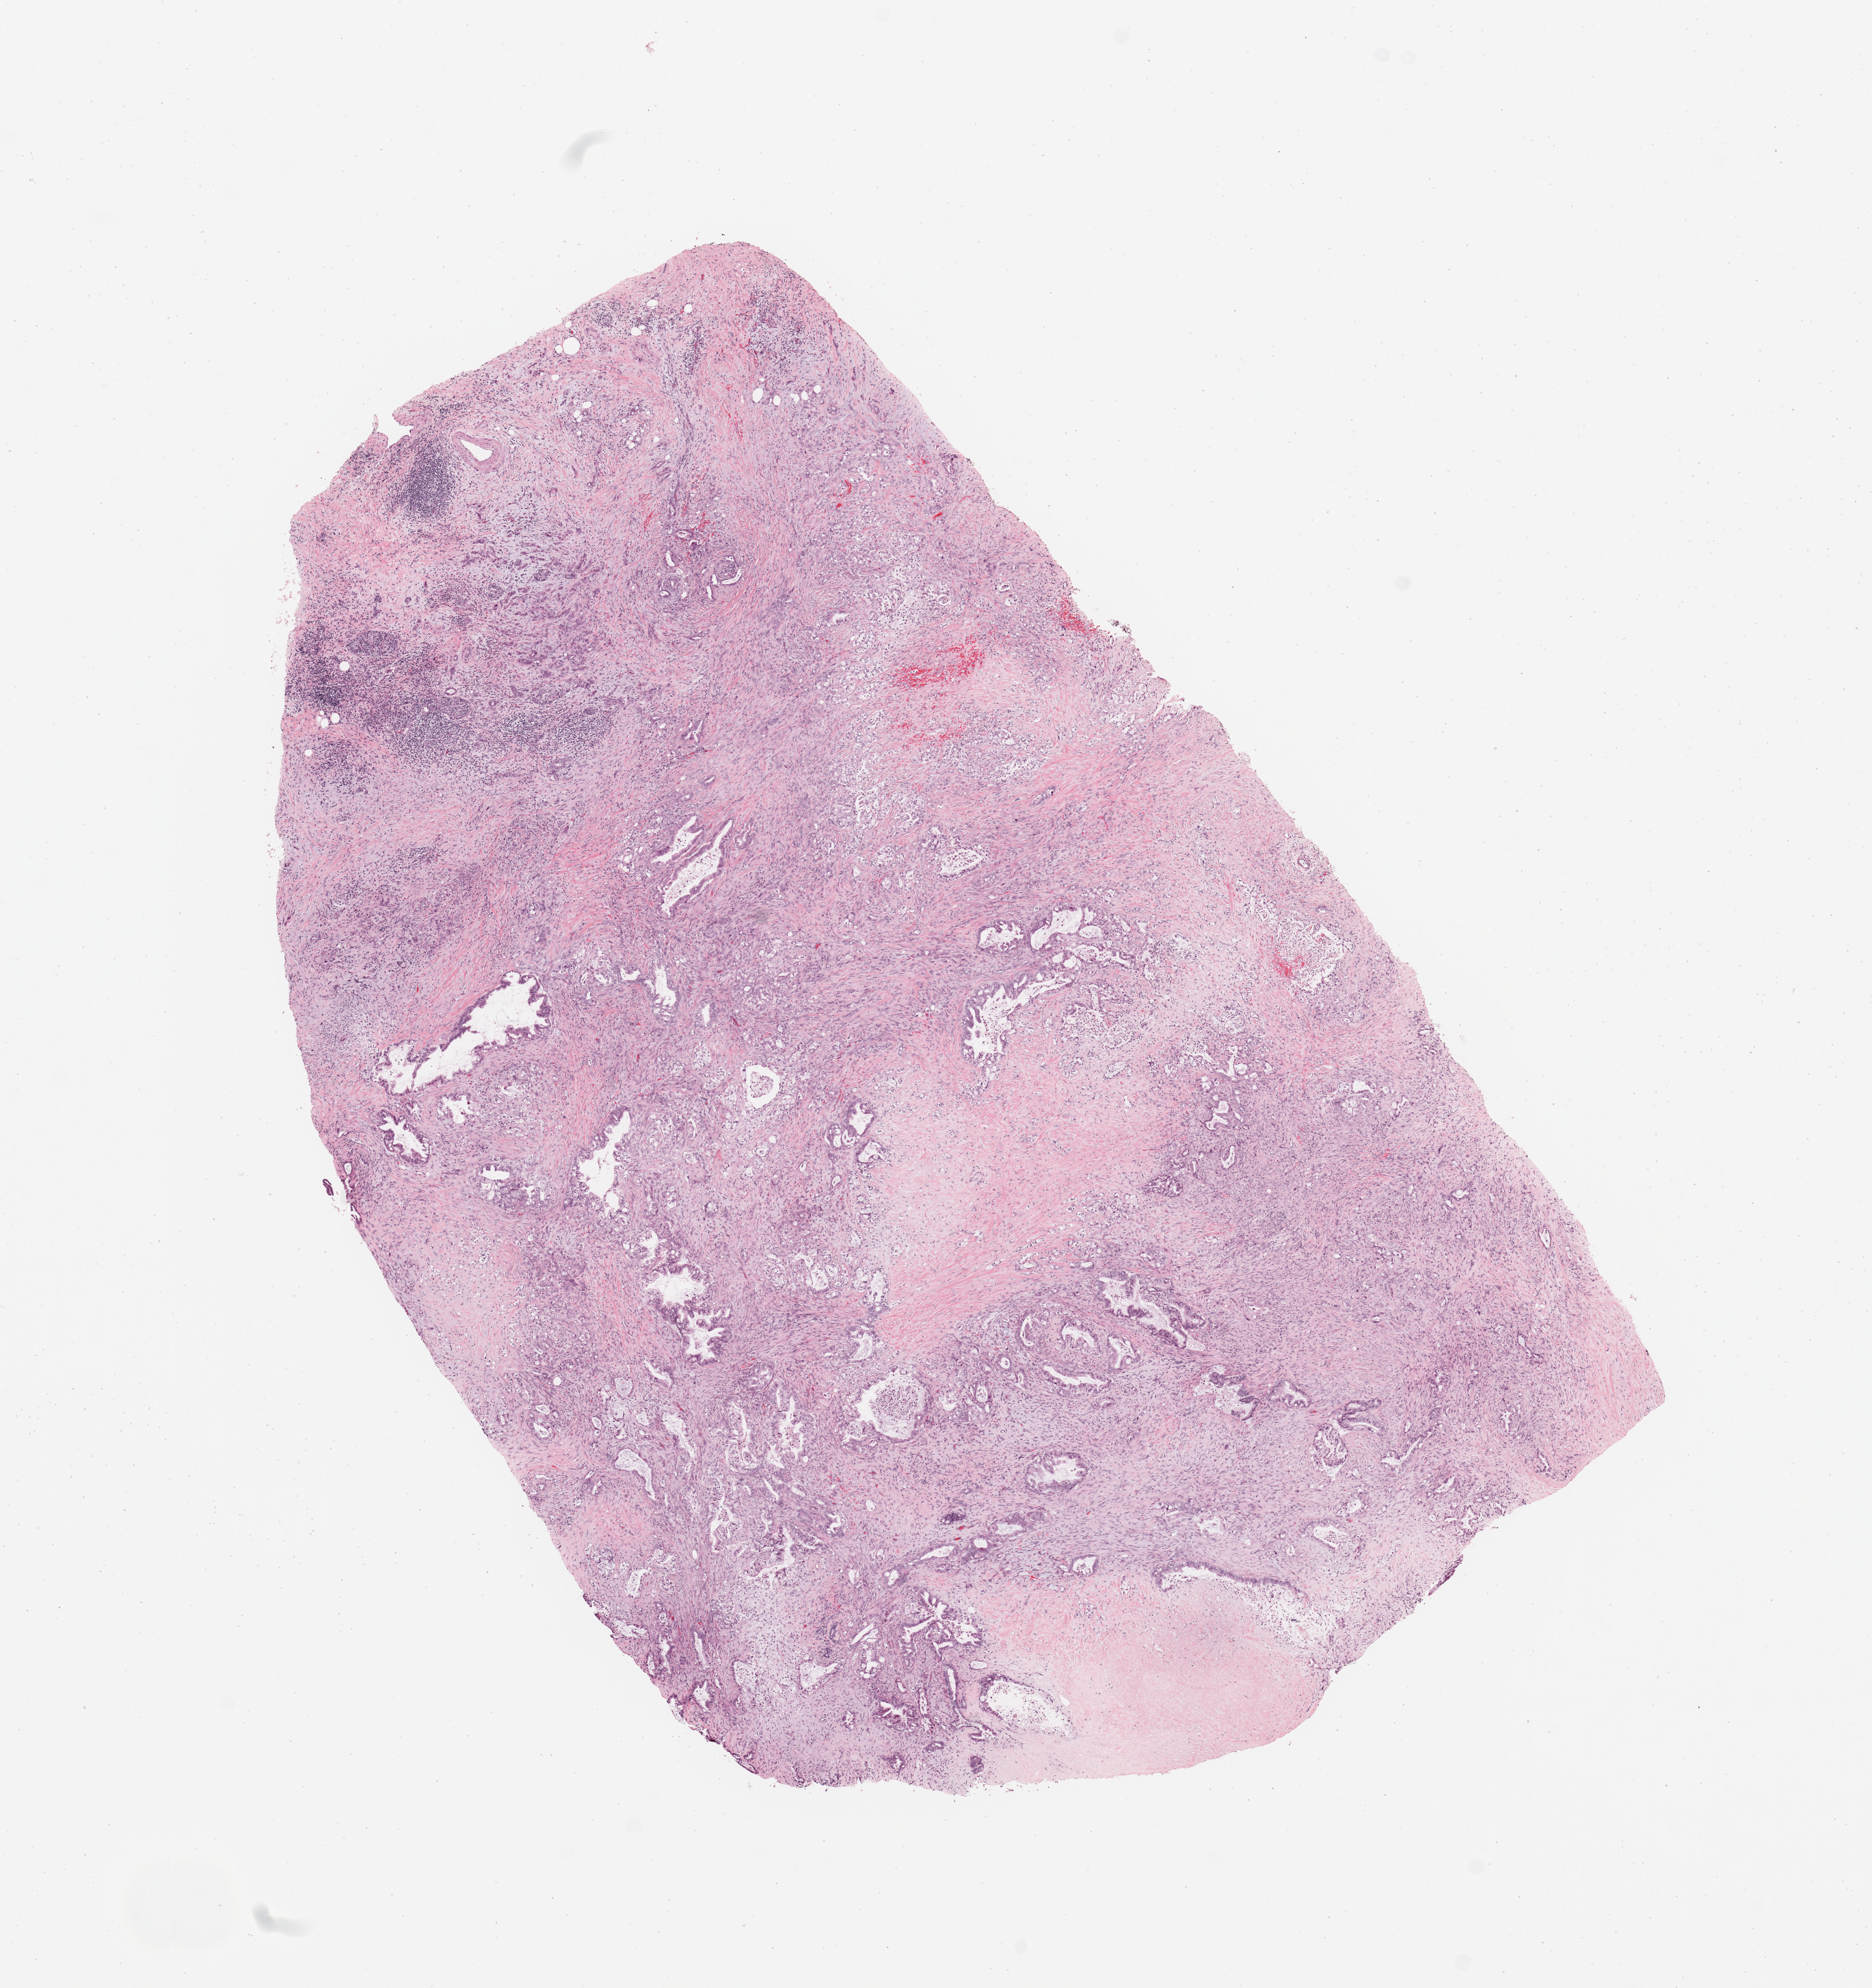
Digitized H&E tissue section (whole slide) — a low-resolution overview of the entire scanned area, about 10.8 x 11.5 mm (acquisition: 20x scan). Tumour tissue sample, sampled site: pancreas. Male, 73 y/o. Histologic grade: G2 (moderately differentiated). Composition of this section per pathologist review: tumour nuclei 60%, necrosis 10%.
Primary tumour site (as recorded): head. AJCC pathologic stage: IV. Diagnosis: Infiltrating duct carcinoma, NOS.